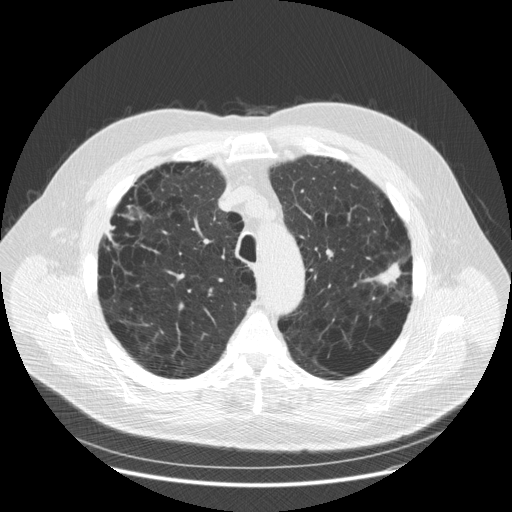
Low-dose screening chest CT, axial slice, baseline annual screen, lung window (W 1500 / L -600 HU), standard (soft-tissue) reconstruction kernel (STANDARD), slice 45 of 179 in the series. Male participant, aged 70 years at enrolment. Current smoker at enrolment.
Expert-annotated lung lesion, box from (x=362, y=248) to (x=418, y=299) px. The exam's reader record, not a measurement of the box and not confirmed to be the same lesion: non-calcified nodule or mass ≥4 mm, left upper lobe, 25 × 13 mm, spiculated (stellate) margins, soft tissue attenuation. Official screen result: positive, change unspecified: nodule(s) >= 4 mm or enlarging nodule(s), mass(es), or other non-specific abnormalities suspicious for lung cancer.